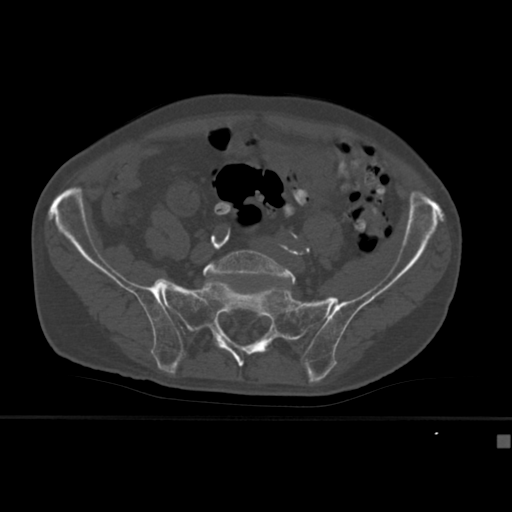
CT including the spine, one axial slice. Slice 72 of 430 in the series (ordered by position). Reconstruction kernel Br40s. Bone window (W 1800 / L 400 HU). 512 × 512 image matrix, field of view 337 × 337 mm. Patient: male, 64 years. Case-level facts recorded for this patient, not image findings: primary cancer: uterus; vertebrae with lytic lesions (as recorded): T1, T4, T5, T7, L5.
Annotated regions visible in this slice (semi-automatically segmented with operator editing):
- L5 vertebra: bounding box <203,250,296,285> (left, top, right, bottom; pixels)